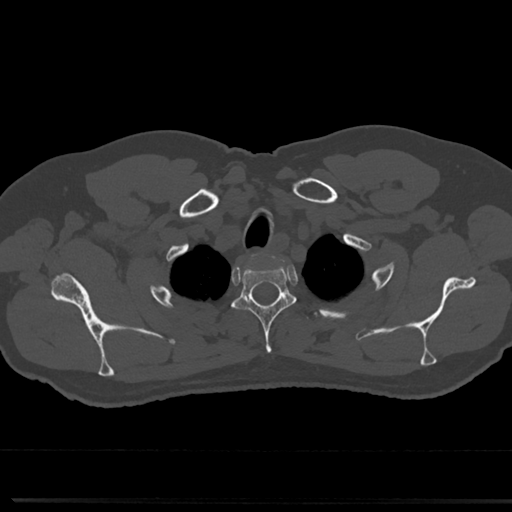
CT including the spine, one axial slice. Position 634 of 817 along the scan axis. Bone window (W 1800 / L 400 HU). 512 × 512 image matrix, field of view 355 × 355 mm. Patient: male, 61 years. From the clinical record (not read from this slice): primary cancer: prostate.
Annotated regions visible in this slice (semi-automatically segmented with operator editing):
- T2 vertebra: bounding box [x1, y1, x2, y2] px = [234, 257, 294, 356]
- T3 vertebra: [297, 312, 311, 325]